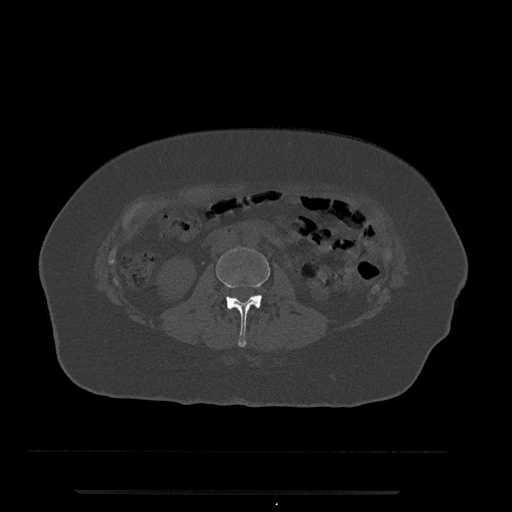
CT including the spine, one axial slice; position 26 of 797 along the scan axis; reconstruction kernel Br40s/3; 120 kVp; bone window (W 1800 / L 400 HU); 0.5 mm slice thickness; 512 × 512 image matrix, field of view 440 × 440 mm. Patient: female, 51 years. From the clinical record (not read from this slice): primary cancer: neuro; vertebrae with lytic lesions (as recorded): T8.
Annotated regions visible in this slice (semi-automatic segmentation, software-assisted and operator-edited):
- L2 vertebra: bounding box [x1, y1, x2, y2] px = [216, 247, 270, 347]